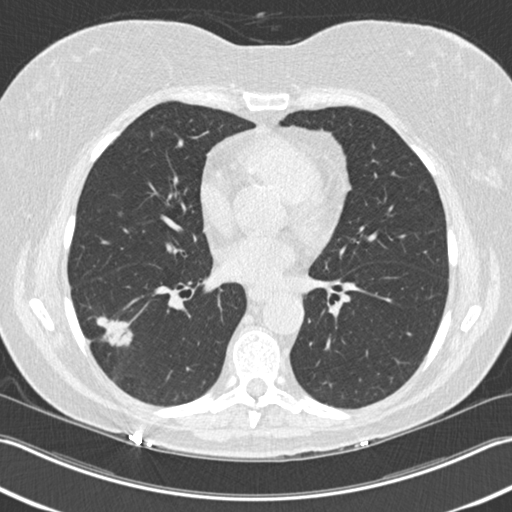
Low-dose screening chest CT, axial slice; baseline annual screen; lung window (W 1500 / L -600 HU); 2 mm slice thickness; standard (soft-tissue) reconstruction kernel (B30f); 120 kVp; slice 101 of 211 in the series. Female, age 63 years at enrolment. Current smoker at enrolment.
- Expert reader's lesion annotation, bounding box (x1, y1, x2, y2) in pixels: (71, 310, 135, 370).
- The screening reader recorded 3 non-calcified nodules or masses ≥4 mm on this exam (right upper lobe, right lower lobe, right lower lobe); which of them this box marks is not recorded.
- Official screen result: positive, change unspecified: nodule(s) >= 4 mm or enlarging nodule(s), mass(es), or other non-specific abnormalities suspicious for lung cancer.
- Later outcome: lung cancer diagnosed 57 days after this screen — bronchiolo-alveolar adenocarcinoma, NOS, right lower lobe, well differentiated (G1), stage IA (AJCC 6th edition), 25 mm at pathology.